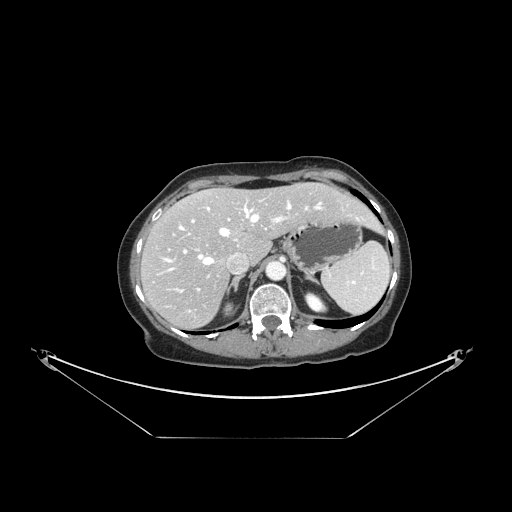
Contrast-enhanced abdominal CT, one axial slice. Slice 107 of 148 in the series (ordered by position). Reconstruction kernel STANDARD. 120 kVp. Intravenous contrast given. Soft-tissue window (W 400 / L 40 HU). 512 × 512 image matrix, field of view 500 × 500 mm. Female patient, age 73 years. From the clinical record (not read from this slice): diagnosis: colorectal cancer liver metastases, imaged before liver resection; multiple liver metastases: no; largest metastasis: 1 cm; disease in both lobes: no.
Structures marked on this image (manually delineated by an expert):
- hepatic veins: bounding box <164,201,359,270> (left, top, right, bottom; pixels)
- liver: <143,184,378,328>
- planned liver remnant (the part of the liver to remain after resection): <168,184,377,260>
- portal vein (with intrahepatic branches): <178,204,307,292>